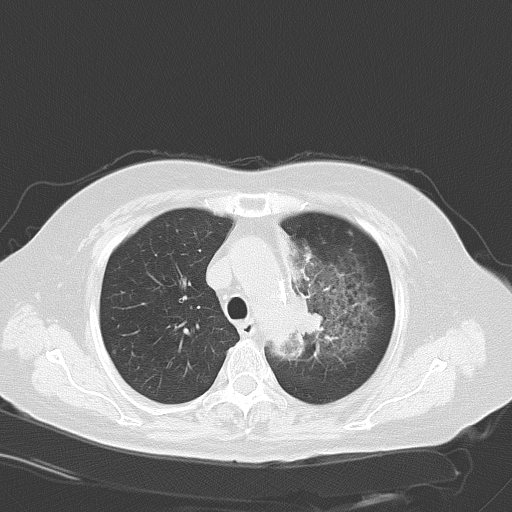
Chest CT, one axial slice; position 42 of 56 along the scan axis; reconstruction kernel B70f; 120 kVp; lung window (W 1500 / L -600 HU); 5 mm slice thickness; 512 × 512 image matrix, field of view 353 × 353 mm. Female patient, age 65 years. Case-level facts recorded for this patient, not image findings: clinical TNM (as recorded): T2b N1 M0.
Annotated regions visible in this slice (rectangle marked by the reading radiologist):
- lung tumour (recorded histology: adenocarcinoma): bounding box [x1, y1, x2, y2] px = [290, 289, 331, 348]